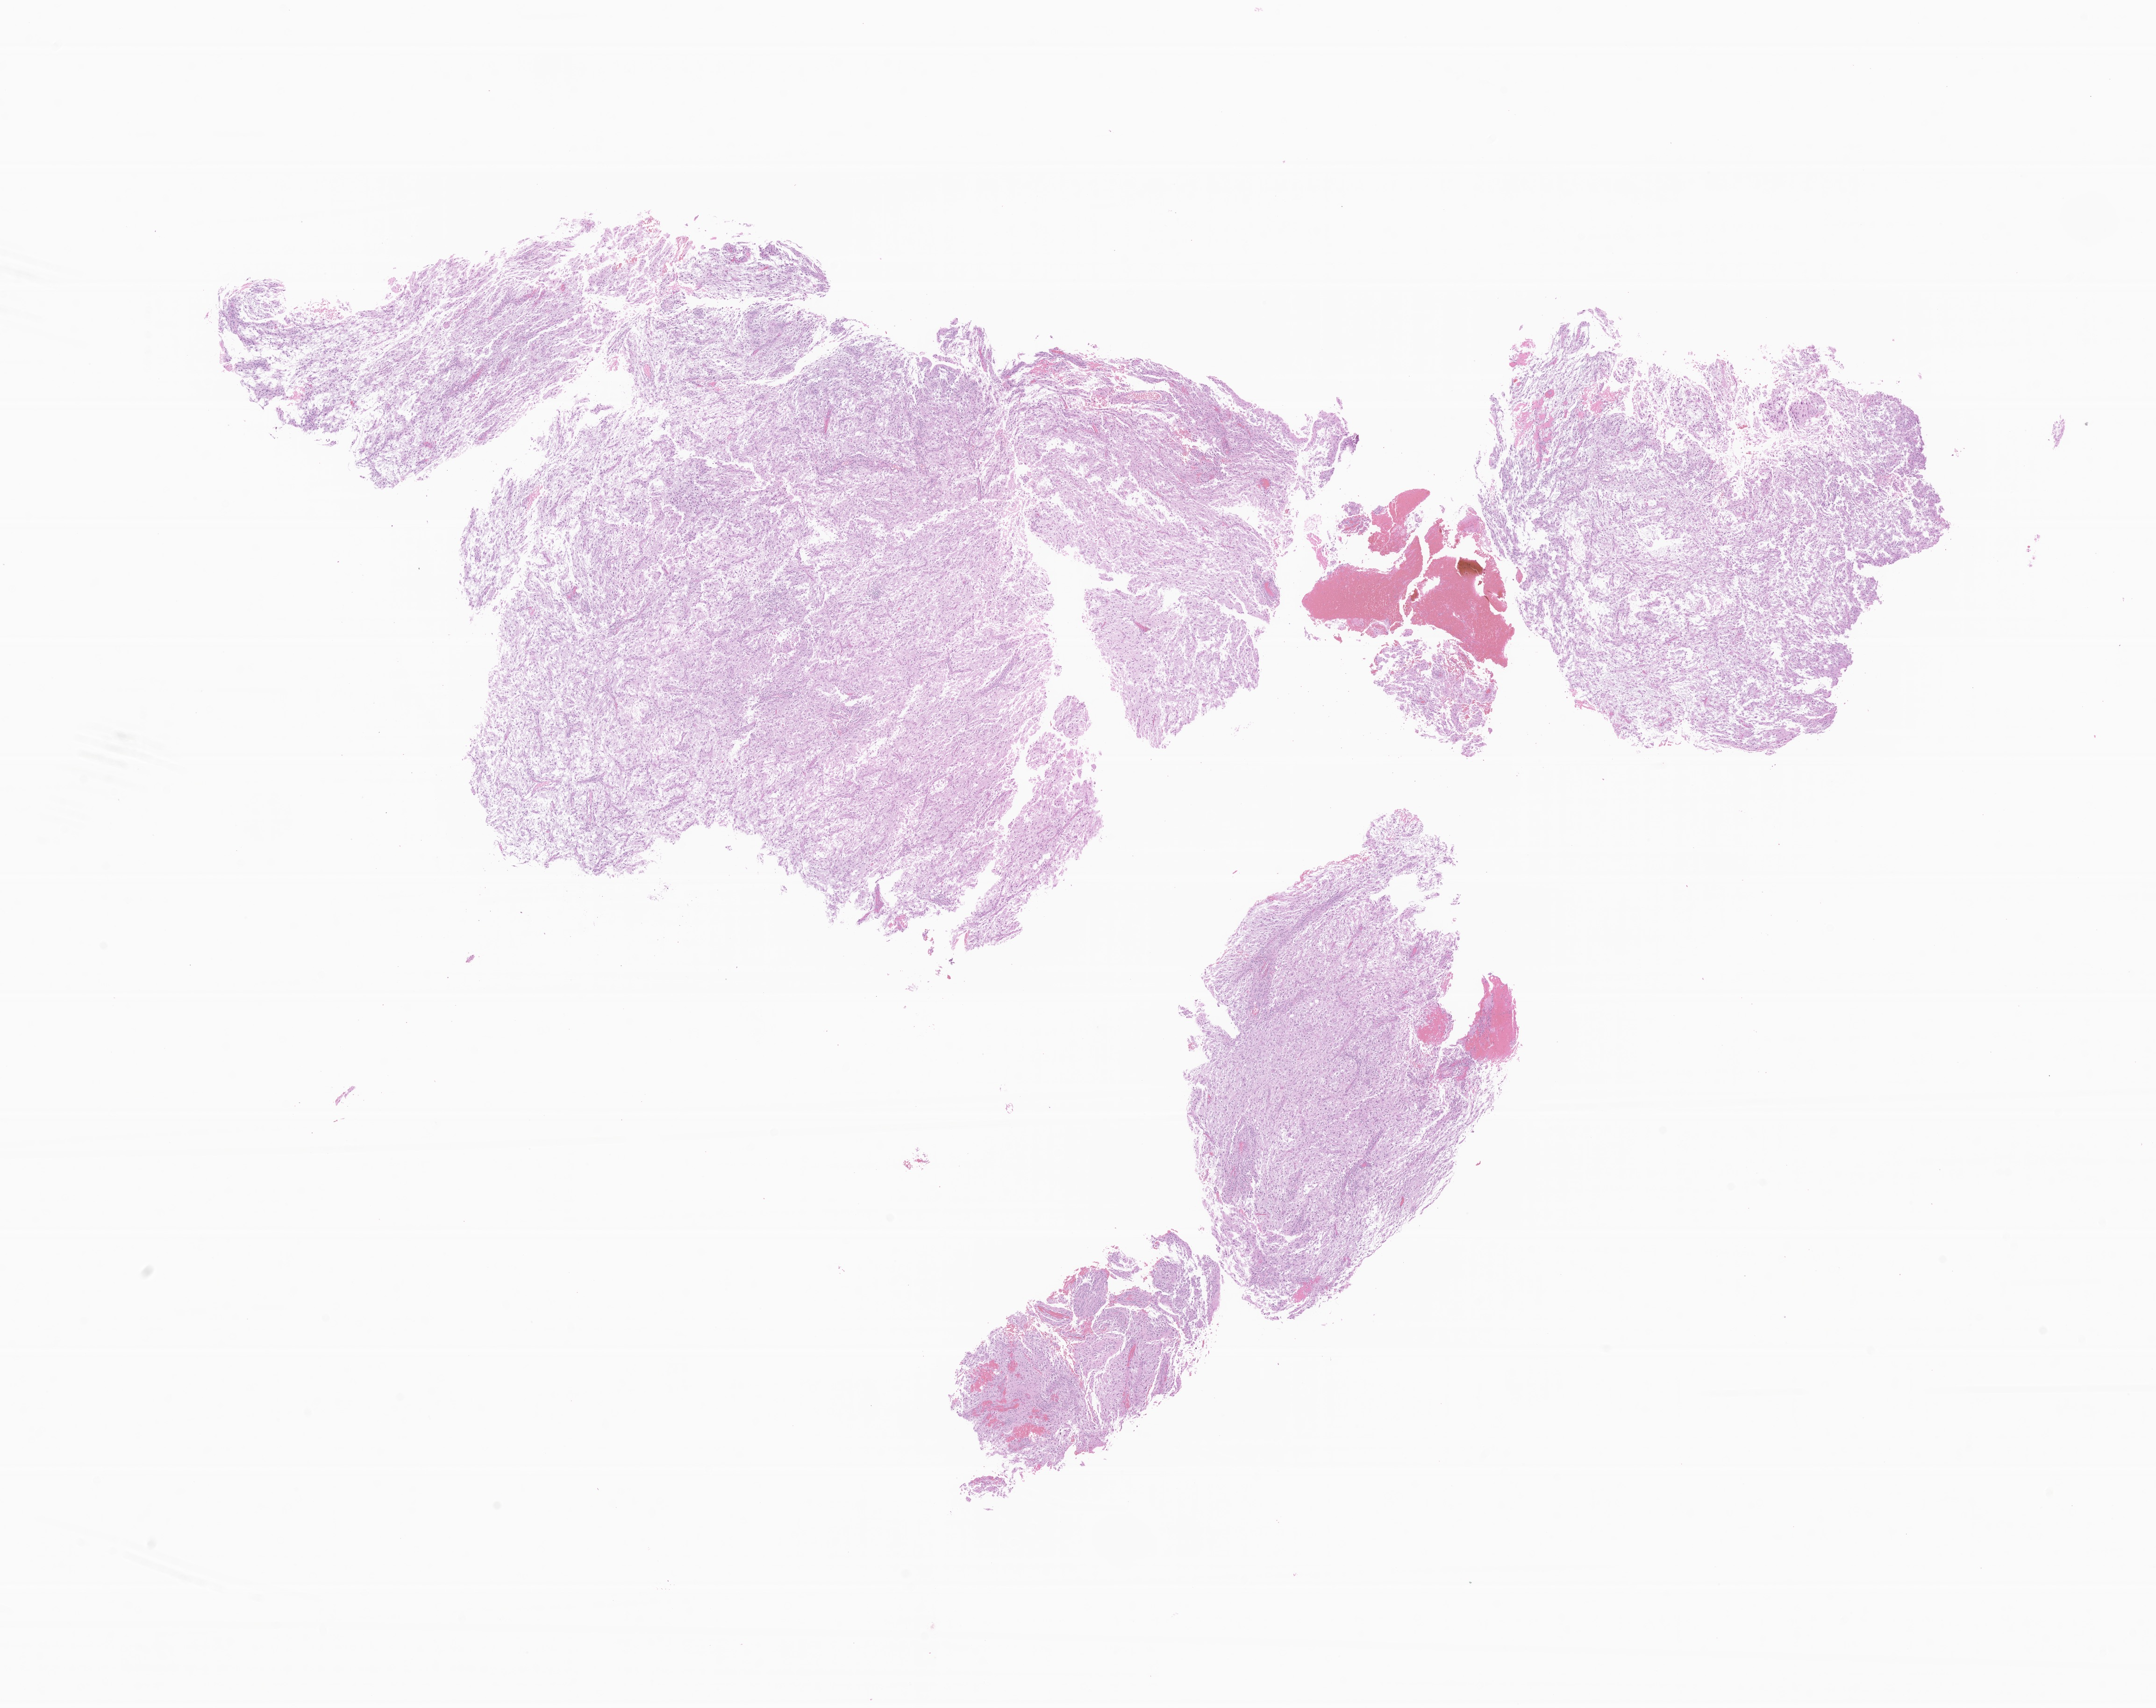
Hematoxylin and eosin (H&E) whole-slide image of tumor tissue from the temporal lobe — shown as a low-resolution overview of the whole scanned area (about 19.5 x 15.4 mm). Formalin-fixed paraffin-embedded section. Patient: male, age 81 months (6 years 9 months).
Diagnosis (ICD-O-3 morphology term): Ganglioglioma, NOS.